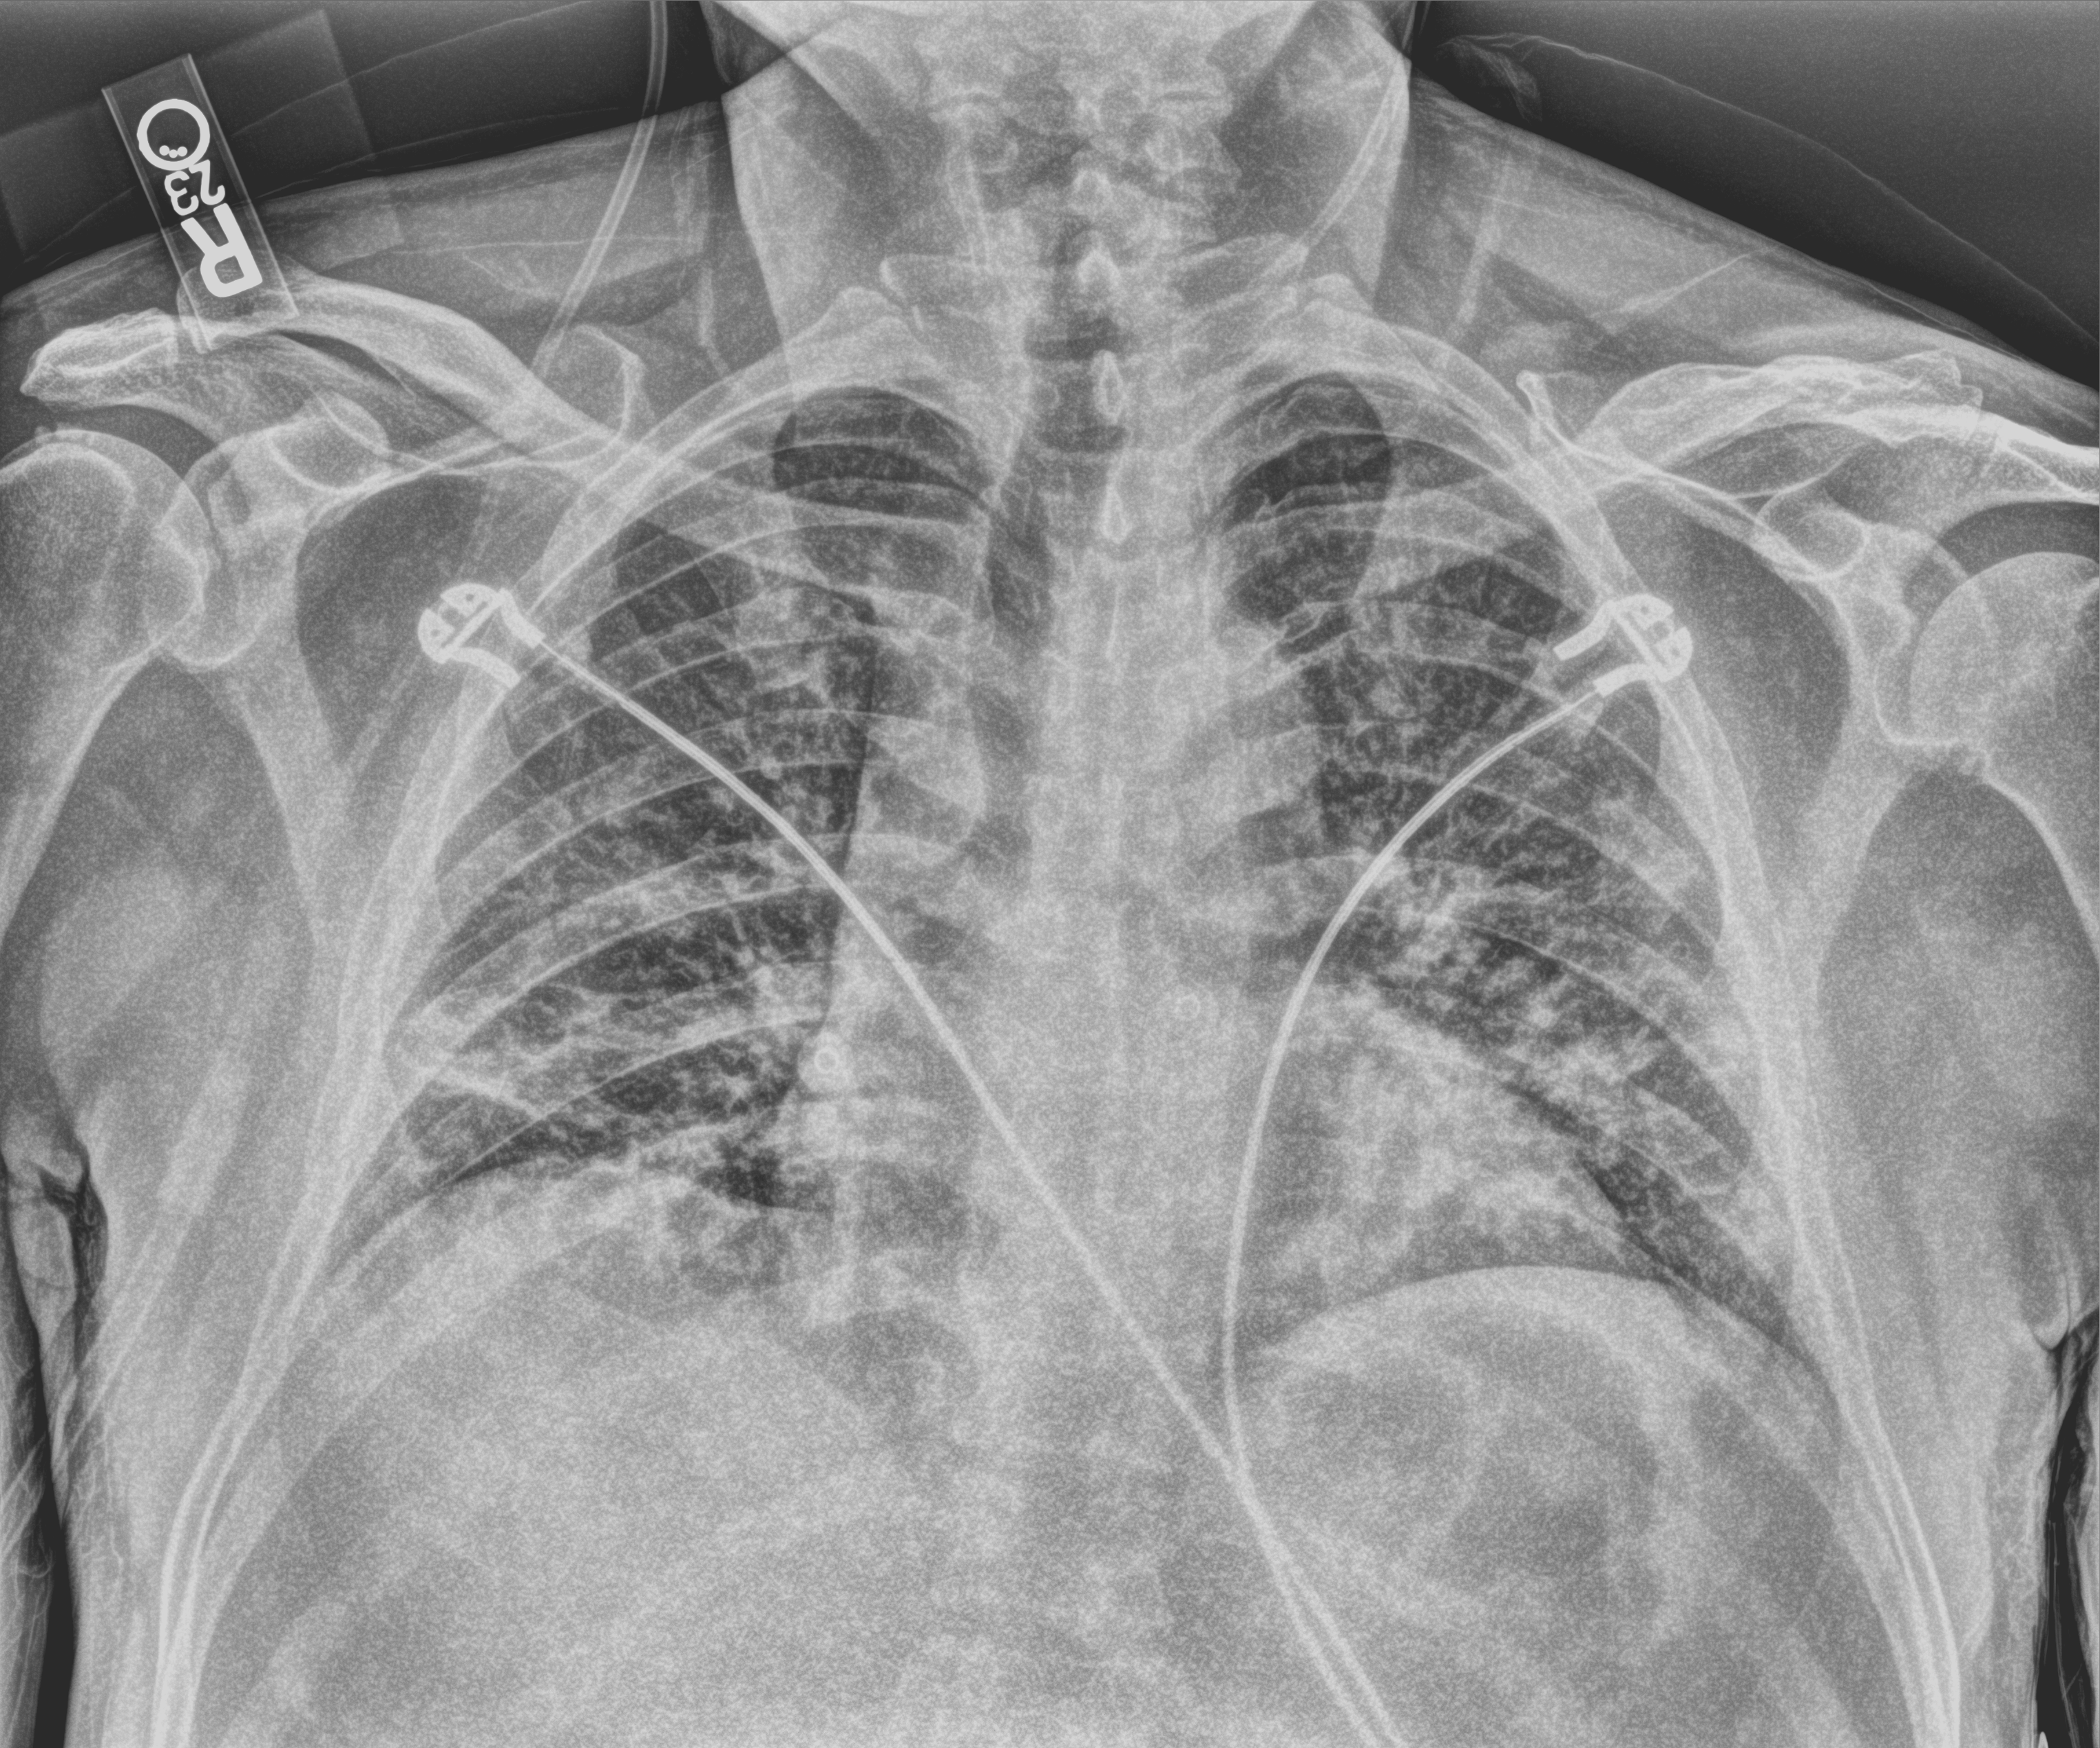
Bedside chest radiograph (computed radiography); anteroposterior (AP) projection. Patient hospitalised with COVID-19; male, aged 18–59 years.
From the hospital-stay record, not from the radiograph (when in the stay this image was taken is not recorded): chronic kidney disease (admission record): no.